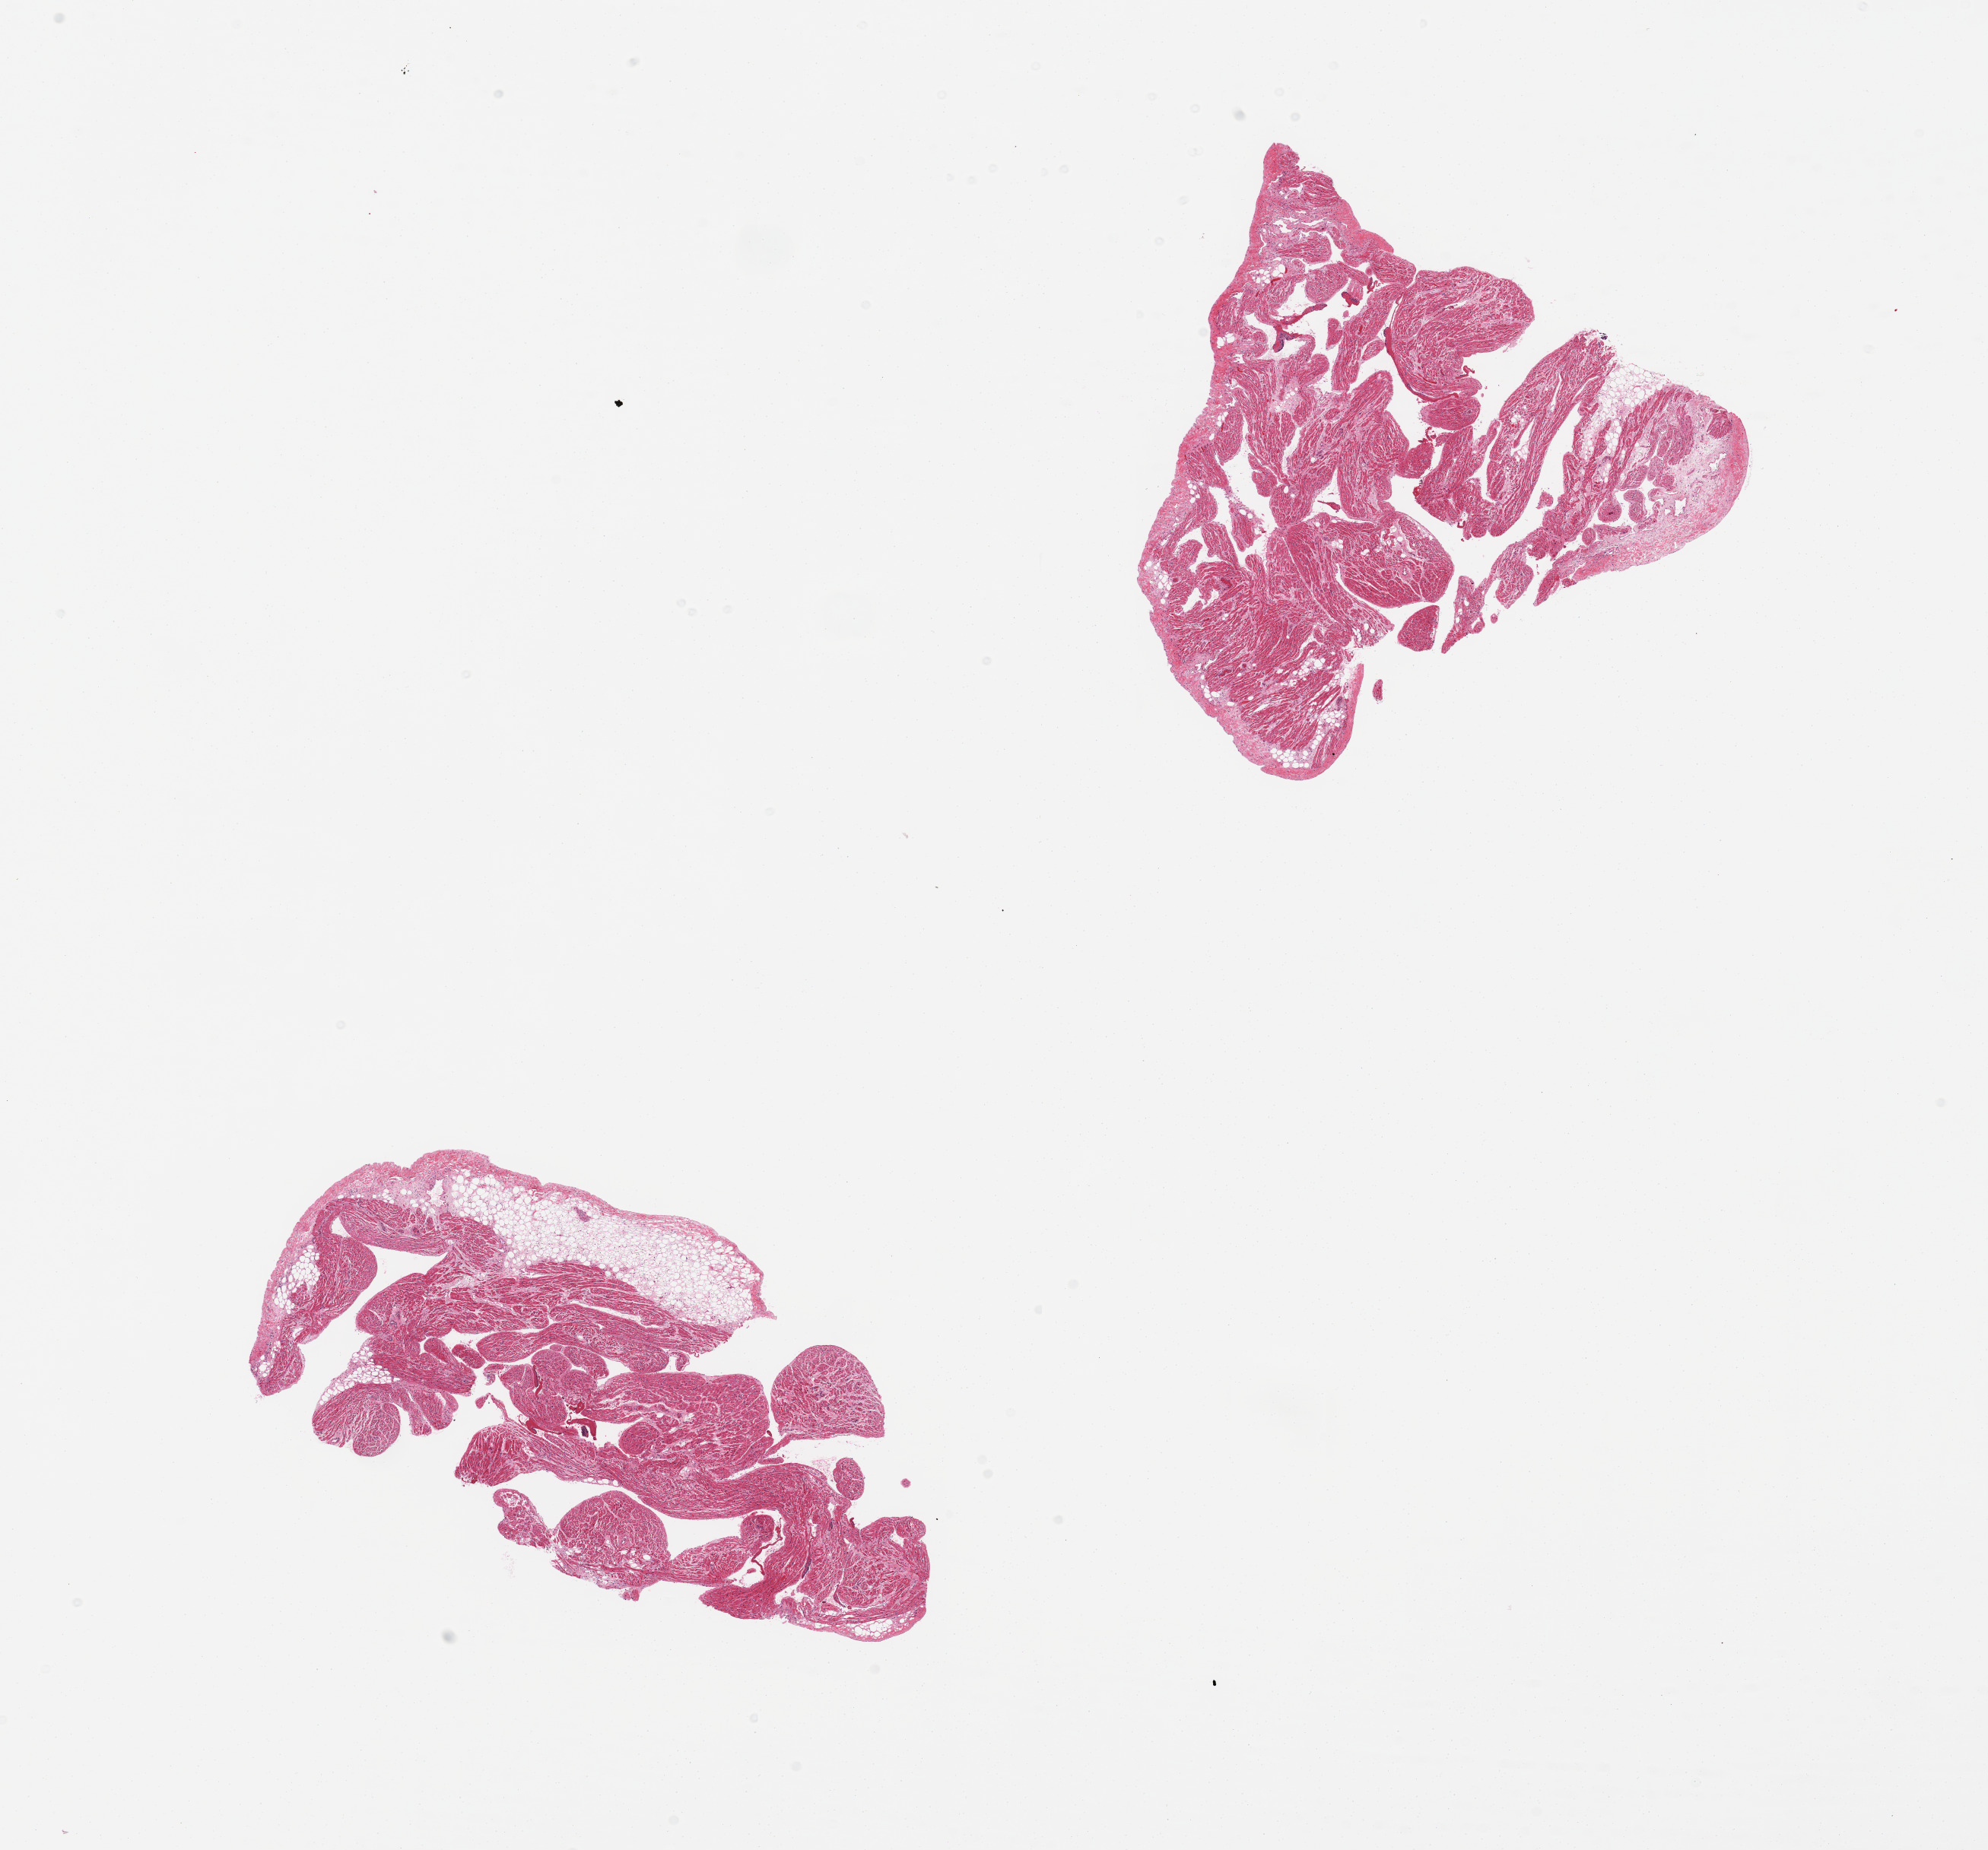
Whole-slide image, H&E stain, a low-resolution overview of the entire scanned area, about 20.7 x 19.2 mm. PAXgene-fixed paraffin-embedded (PFPE) section. Section of auricular appendage (target tissue). Donor tissue sample.
Reviewer comment on this tissue sample: 2 pieces, focal adherent fat, ~0.5 mm.